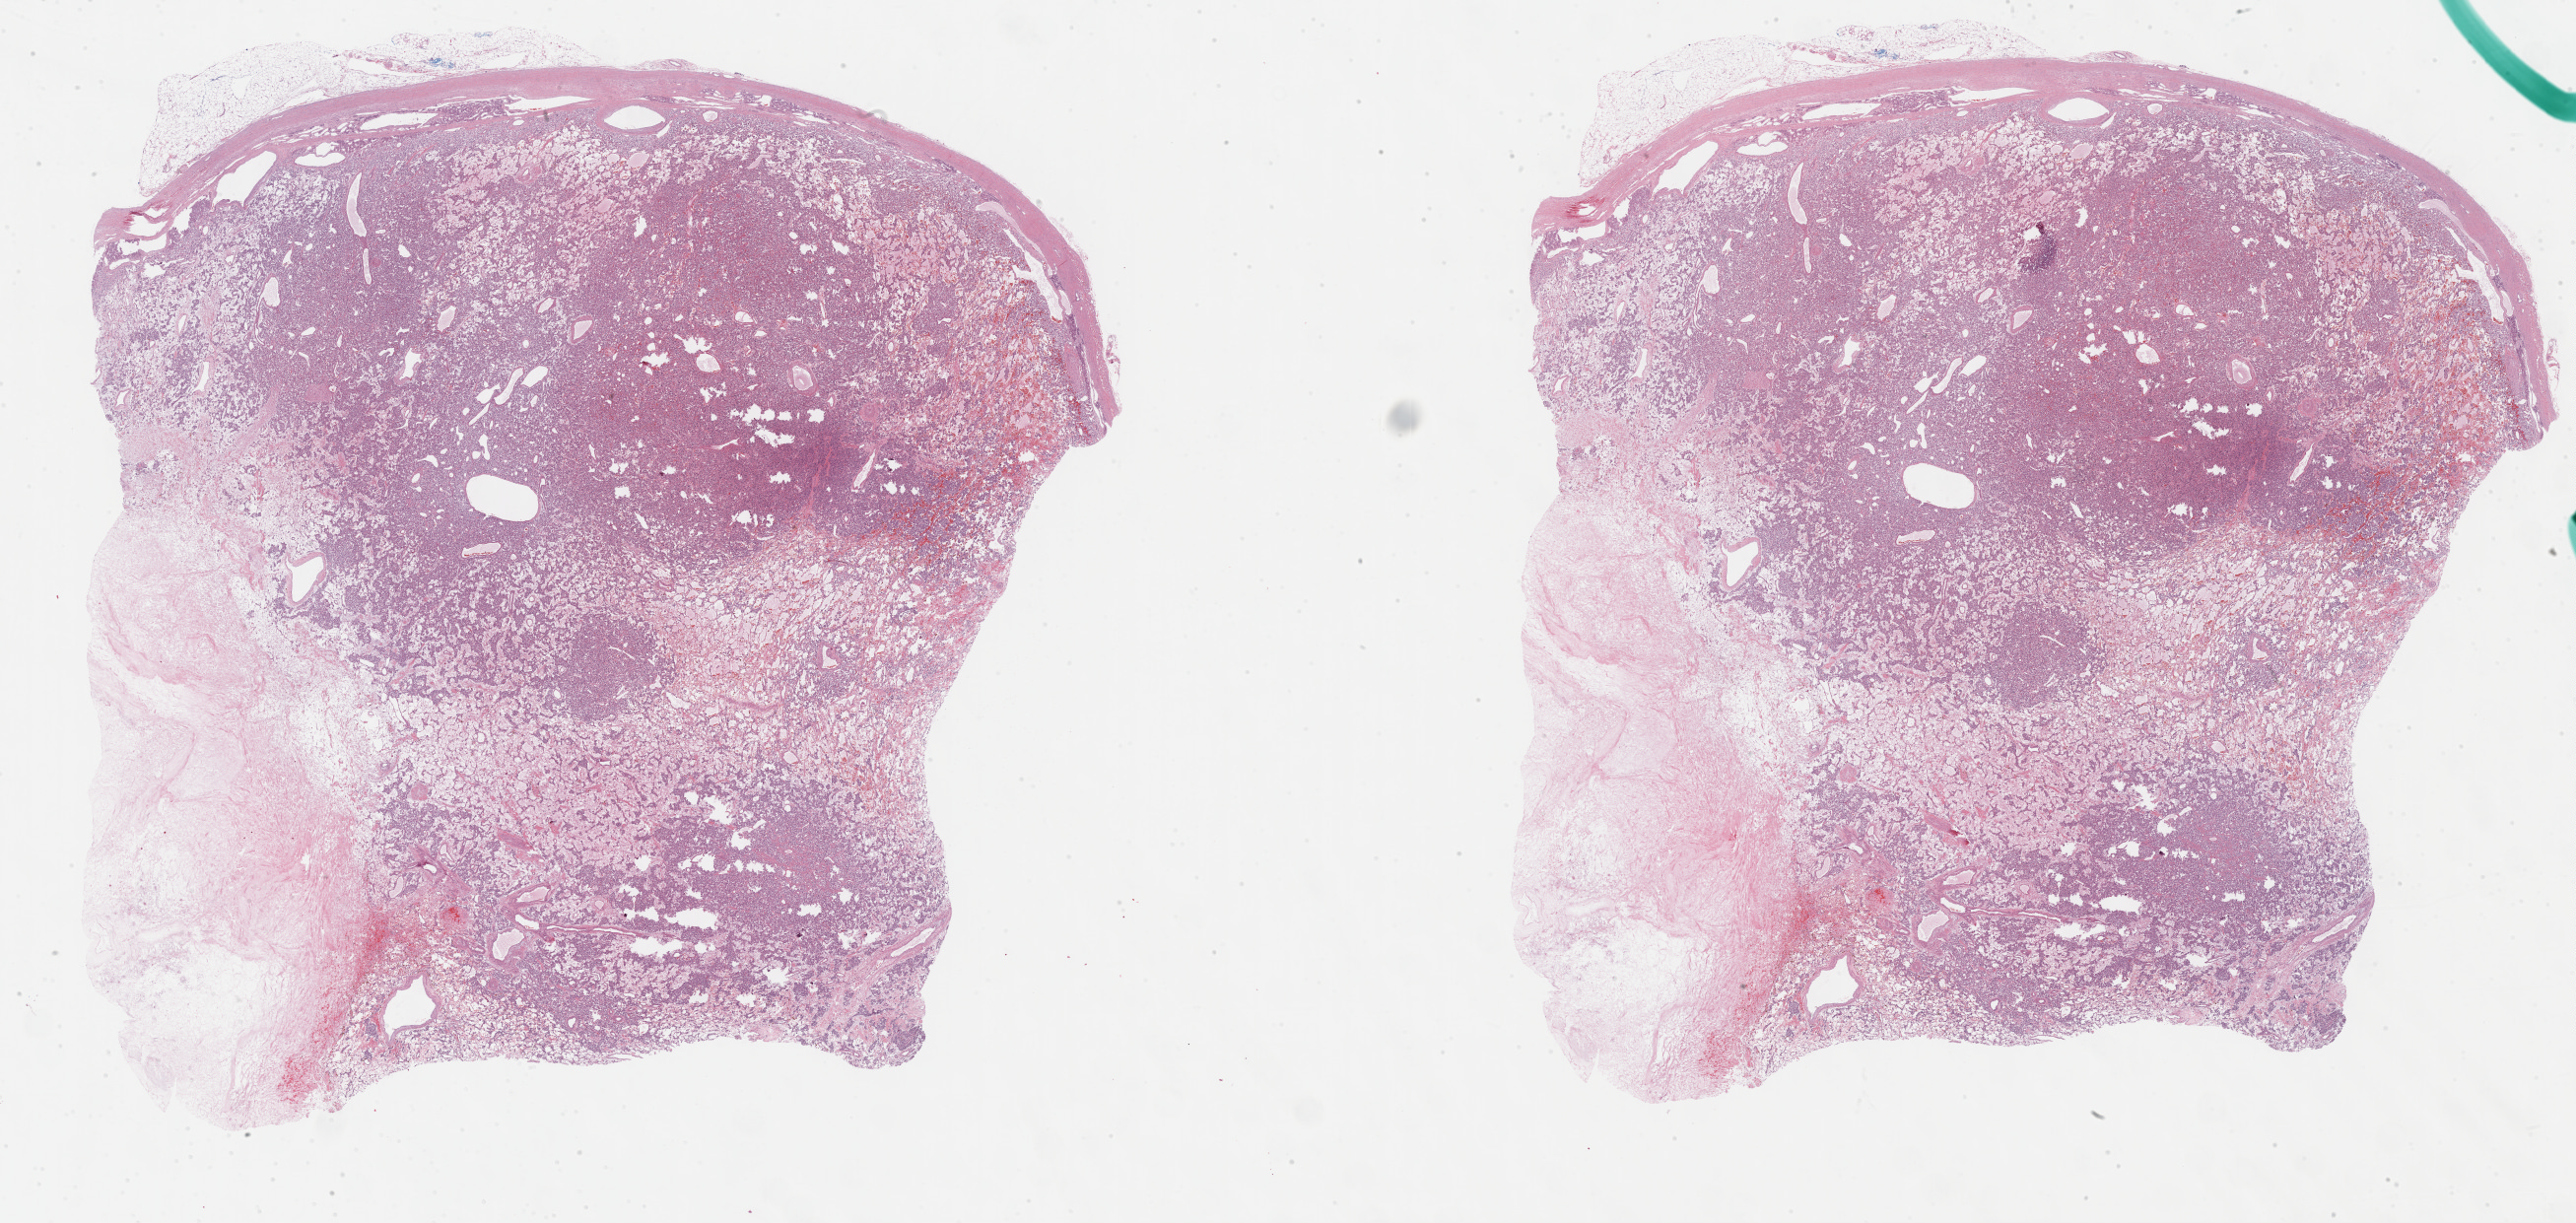
Digitized H&E-stained tissue section (whole slide) — whole scanned area (about 42.3 x 20.1 mm, from a 40x scan) shown as a low-resolution overview; formalin-fixed paraffin-embedded (FFPE) diagnostic section; adrenal gland, primary tumour sample. Male patient; age at initial diagnosis 43 years.
Diagnosis: Pheochromocytoma, NOS.